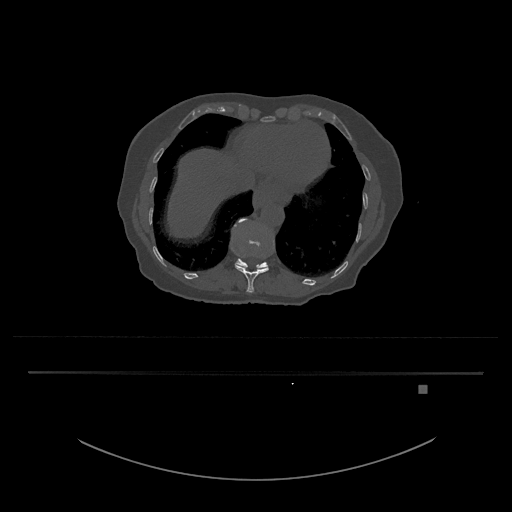
CT including the spine, one axial slice; slice 646 of 797 in the series (ordered by position); 120 kVp; bone window (W 1800 / L 400 HU); 0.5 mm slice thickness; 512 × 512 image matrix. Female patient, age 57 years. Case-level facts recorded for this patient, not image findings: primary cancer: cervical.
Annotated regions visible in this slice (semi-automatic segmentation, software-assisted and operator-edited):
- T11 vertebra: bounding box (x1, y1, x2, y2) in pixels: (232, 219, 269, 293)
- T12 vertebra: (234, 218, 268, 270)